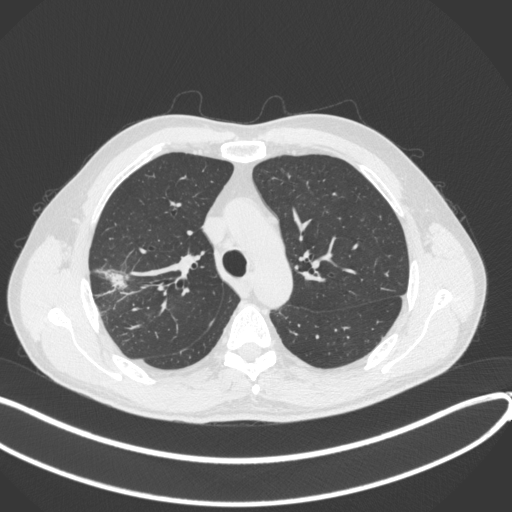
Chest CT, one axial slice; position 300 of 381 along the scan axis; 120 kVp; lung window (W 1500 / L -600 HU); 1 mm slice thickness; 512 × 512 image matrix. Patient: male, 62 years. Case-level facts recorded for this patient, not image findings: clinical TNM (as recorded): T1c N0 M0.
Annotated regions visible in this slice (rectangle marked by the reading radiologist):
- lung tumour (recorded histology: adenocarcinoma): bounding box (x1, y1, x2, y2) in pixels: (98, 262, 131, 293)